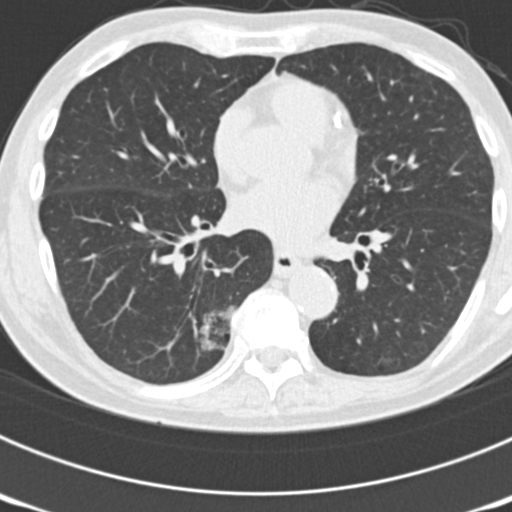
Chest CT (low-dose screening protocol), one axial image; third screening round (two years after baseline); lung window (W 1500 / L -600 HU); 2 mm slice thickness; slice 88 of 177 in the series; 512 × 512 image matrix, field of view 300 × 300 mm. Male, age 70 years at enrolment. Current smoker at enrolment.
Expert reader's lesion annotation, bounding box <149,299,239,384> (left, top, right, bottom; pixels). The screening reader recorded 3 non-calcified nodules or masses ≥4 mm on this exam (right upper lobe, left upper lobe, right lower lobe); which of them this box marks is not recorded. Participant outcome: lung cancer diagnosed 14 days after this screen — bronchiolo-alveolar adenocarcinoma, NOS, right lower lobe, poorly differentiated (G3), stage IB (AJCC 6th edition), 30 mm at pathology.